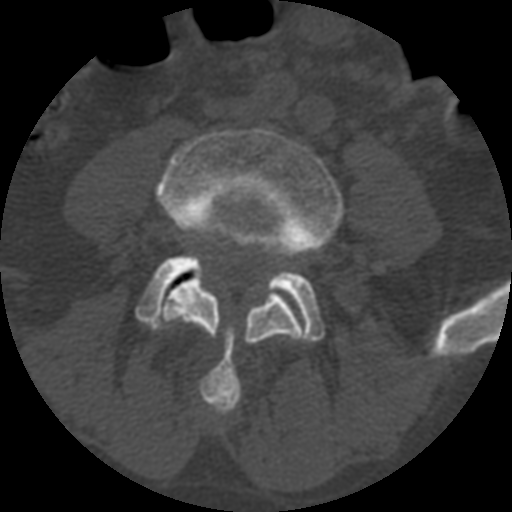
CT including the spine, one axial slice. Slice 271 of 399 in the series (ordered by position). Reconstruction kernel STANDARD. 120 kVp. Bone window (W 1800 / L 400 HU). 1.25 mm slice thickness. 512 × 512 image matrix, field of view 160 × 160 mm. Patient age 71 years. From the clinical record (not read from this slice): primary cancer: prostate.
Annotated regions visible in this slice (semi-automatically segmented with operator editing):
- L4 vertebra: bounding box (x1, y1, x2, y2) in pixels: (157, 127, 343, 414)
- L5 vertebra: (136, 255, 325, 341)